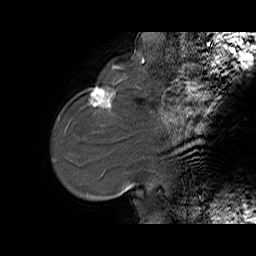
Breast MRI (dynamic contrast-enhanced), one sagittal slice. Slice 14 of 65 in the series (ordered by position). Dynamic contrast-enhanced series, time point 2 of 6 at this slice position (early post-contrast). 1.5 T. TE 5.7 ms, TR 32.9 ms. 256 × 256 image matrix, field of view 230 × 230 mm. Female patient. From the clinical record (not read from this slice): setting: breast cancer imaged before/during neoadjuvant chemotherapy; receptor status: HER2-positive.
Annotated regions visible in this slice (semi-automatically segmented with operator editing):
- analysis volume of interest (the breast-tissue region the enhancement analysis was run in; not a lesion): bounding box [x1, y1, x2, y2] px = [76, 77, 125, 128]
- tumour enhancement mask (voxels above the 100 % enhancement threshold inside the analysis volume of interest): [90, 88, 115, 108]